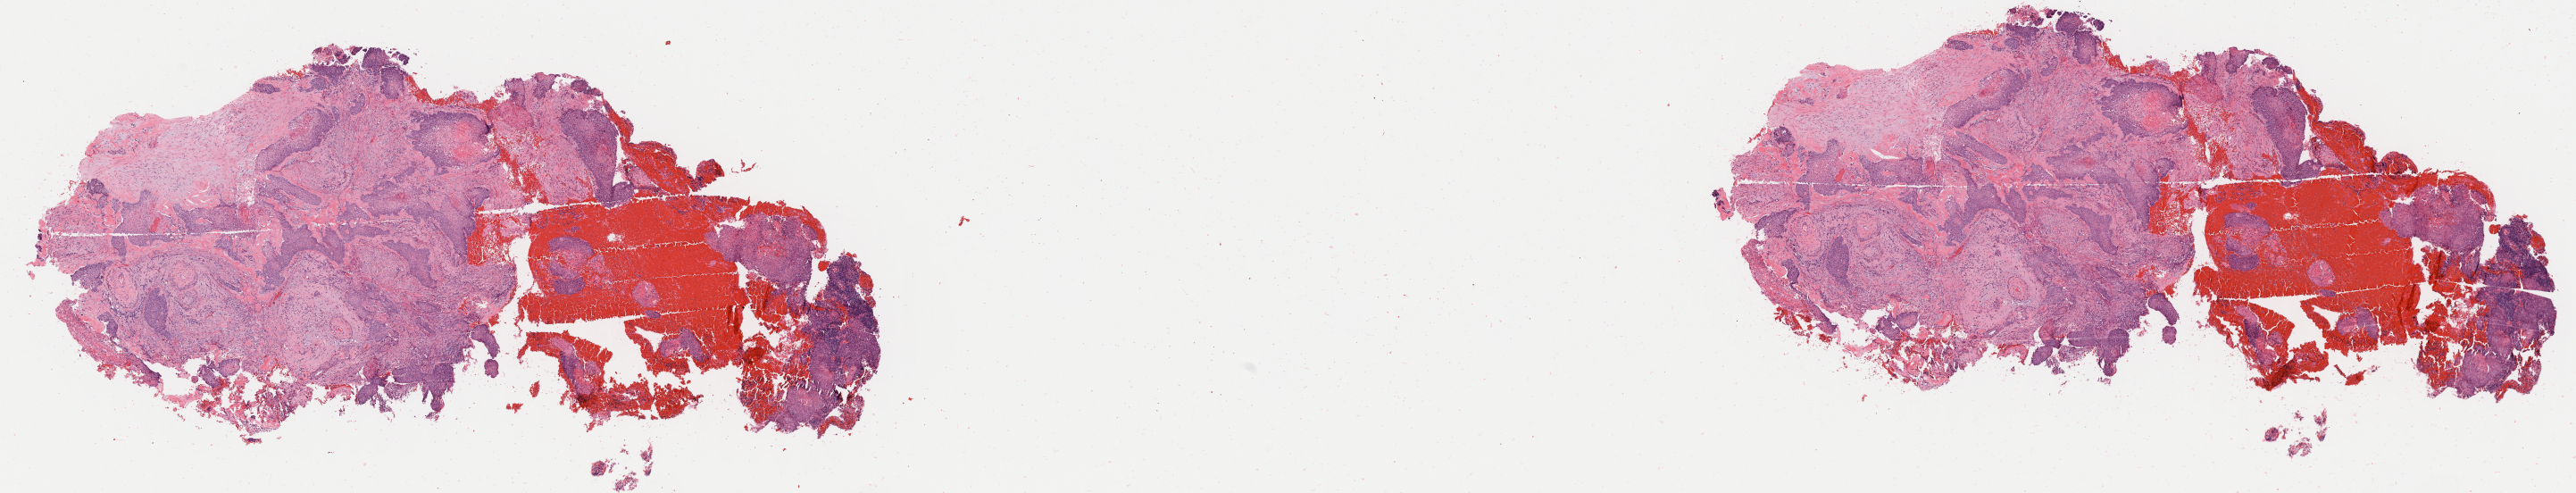
Haematoxylin and eosin whole-slide image, shown as a low-resolution overview of the whole scanned area (about 23.0 x 4.4 mm), specimen: tumor tissue, anatomic site: cervix. Patient female; aged 54.
Histologic diagnosis: Squamous cell carcinoma, keratinizing, NOS.